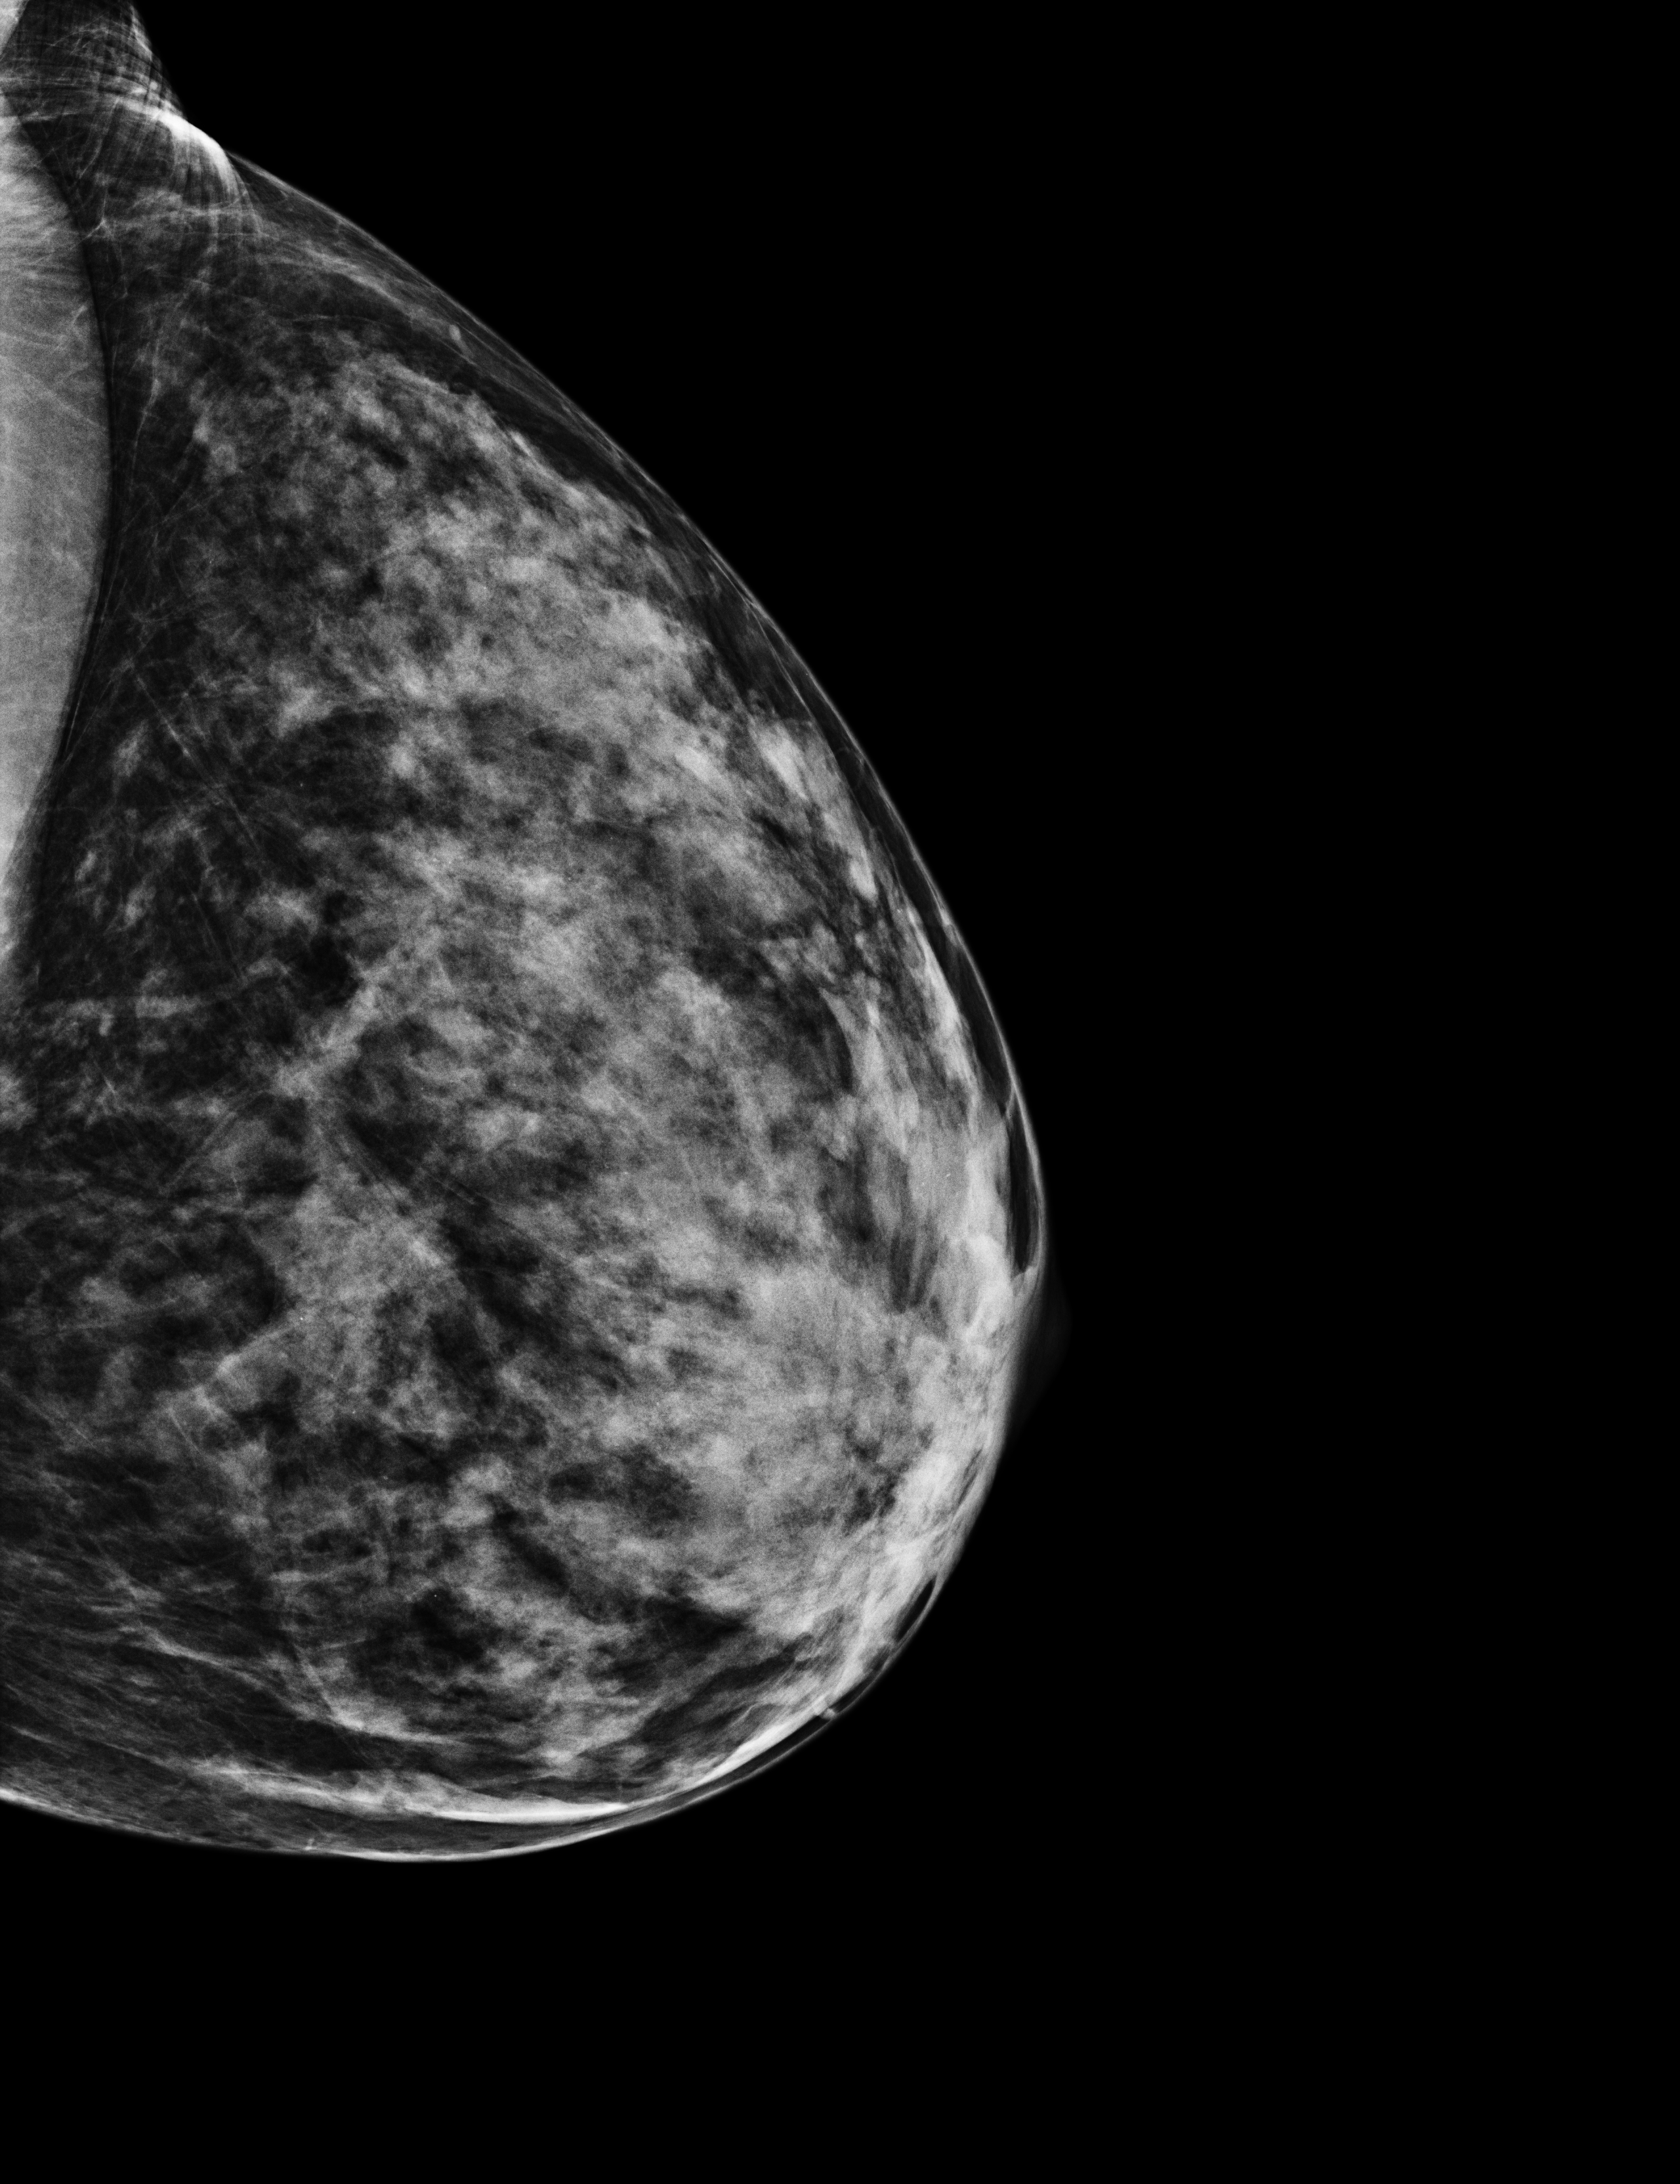
Annual screening mammography examination; system: Selenia Dimensions. Patient aged 44 years (female).
Image type: full-field digital mammogram. Breast: left. Projection: laterally exaggerated craniocaudal (XCCL) view.